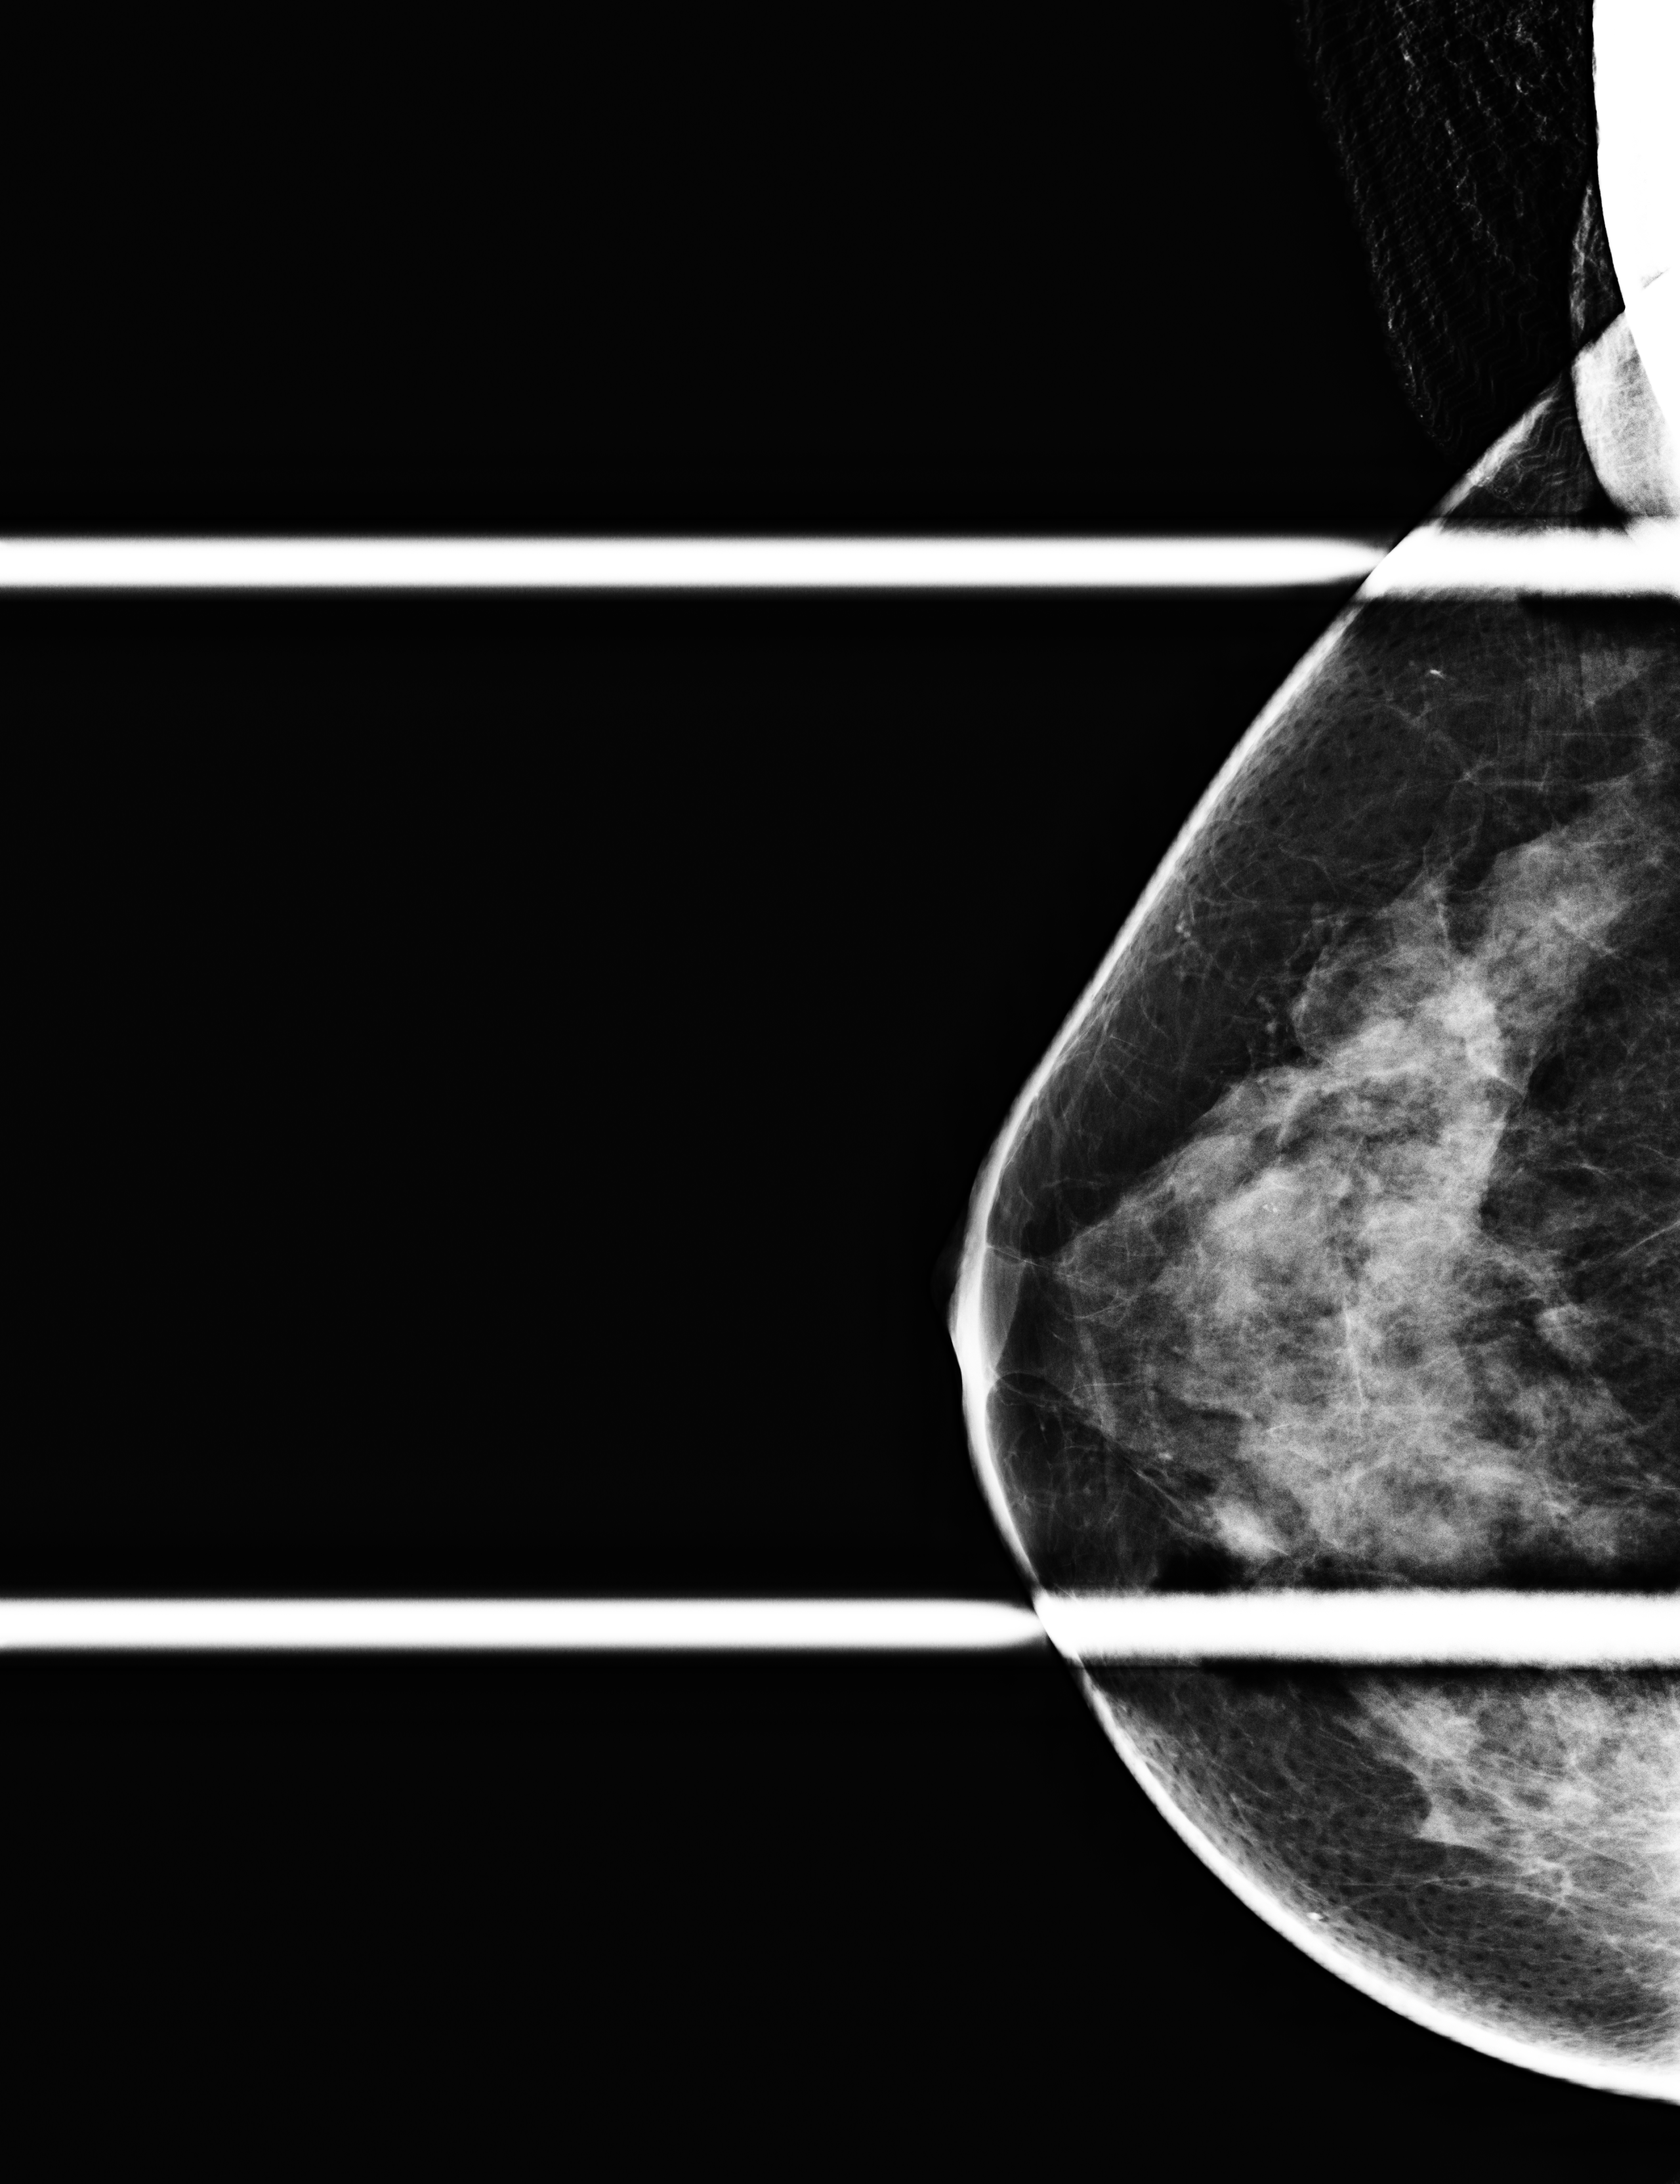
Additional (diagnostic) view; compressed breast thickness 53 mm. Patient aged 58 years (female).
Image type: full-field digital mammogram. Breast: right. Projection: cranio-caudal projection, spot compression. Breast density at the screening exam (both breasts): heterogeneously dense (BI-RADS density category c). Final BI-RADS assessment for this screening round (tomosynthesis exam, both breasts): category 4. Recall: recalled for additional imaging after this screen.